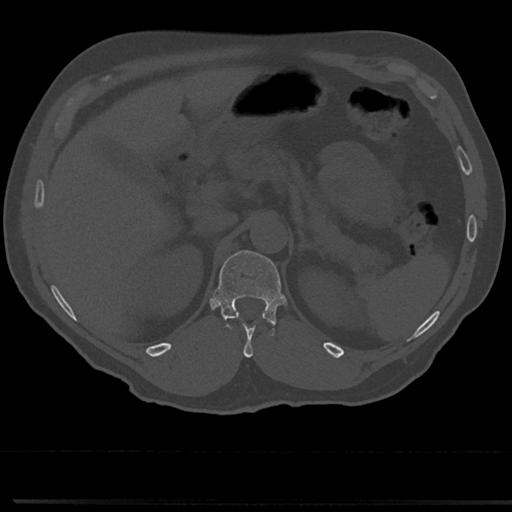
CT including the spine, one axial slice; position 164 of 817 along the scan axis; reconstruction kernel Br40s/3; 120 kVp; bone window (W 1800 / L 400 HU); 0.5 mm slice thickness; 512 × 512 image matrix, field of view 355 × 355 mm. Male patient, age 61 years. From the clinical record (not read from this slice): primary cancer: prostate.
Outlined on this slice (semi-automatic segmentation, software-assisted and operator-edited):
- T11 vertebra: bounding box <231,324,273,356> (left, top, right, bottom; pixels)
- T12 vertebra: <215,249,284,335>